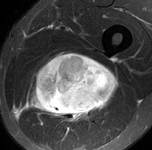
MRI of an extremity soft-tissue mass, one axial slice; STIR; MR volume resampled by the dataset authors to the PET/CT grid (not the native acquisition matrix); 3.27 mm slice thickness; 152 × 150 image matrix, field of view 148 × 146 mm. Male patient. From the clinical record (not read from this slice): histological type: undifferentiated pleomorphic liposarcoma; grade: high; site of the primary tumour: left thigh.
Annotated regions visible in this slice (expert contour drawn on MRI and transferred to this co-registered scan by the dataset authors):
- gross tumour volume including surrounding oedema: bounding box <23,53,119,125> (left, top, right, bottom; pixels)
- gross tumour volume (mass): <32,53,119,117>